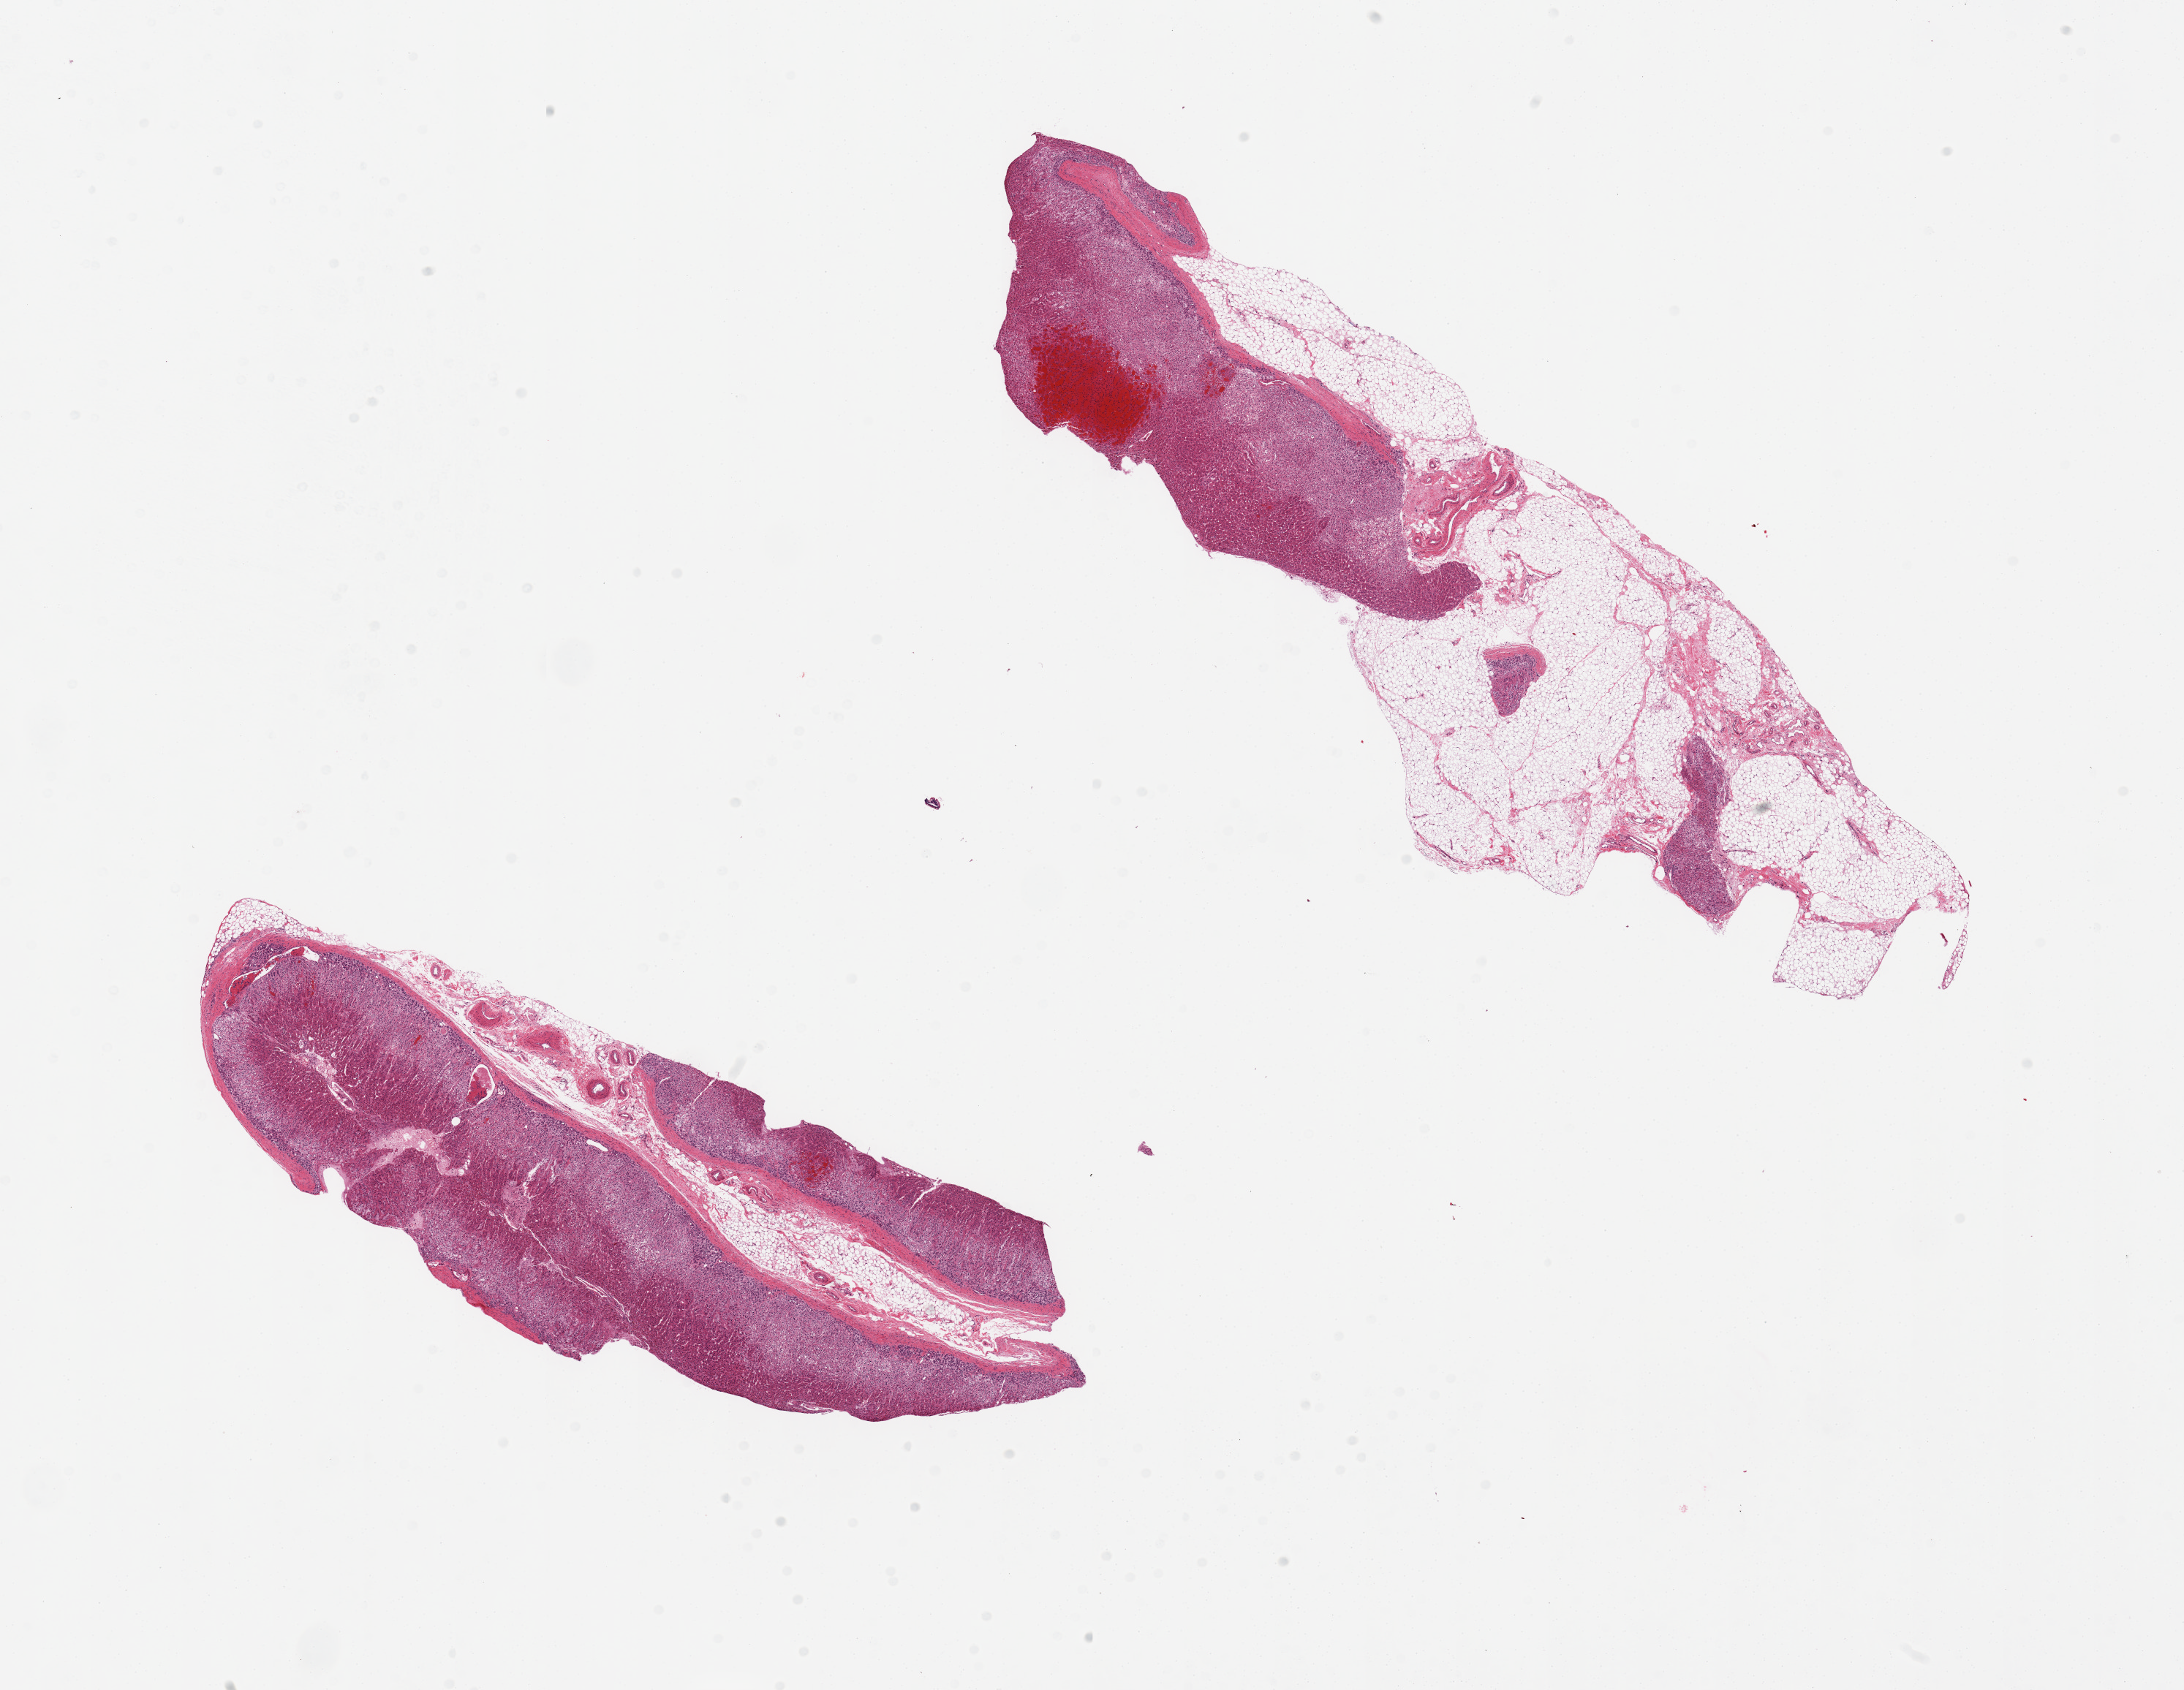
Digitized haematoxylin and eosin-stained section — shown as a low-resolution overview of the whole scanned area (about 23.6 x 18.3 mm, slide scanned at 20x). PAXgene-fixed, paraffin-embedded tissue. Target tissue: adrenal gland. Donor tissue sample. Female donor.
Reviewer comment on this tissue sample: 2 pieces; one 60% fat, other 20%.